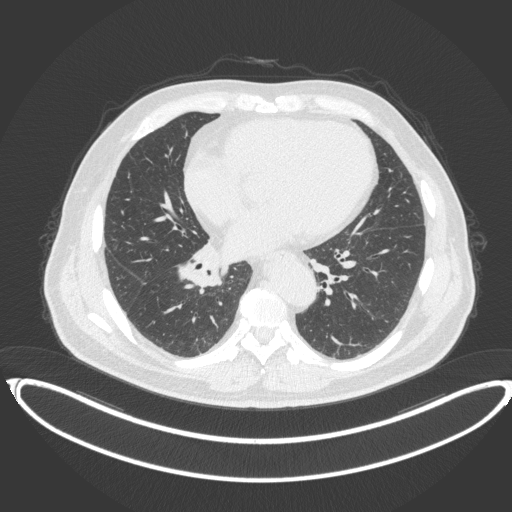
Chest CT, one axial slice. Position 172 of 383 along the scan axis. Lung window (W 1500 / L -600 HU). 1 mm slice thickness. 512 × 512 image matrix, field of view 448 × 448 mm. Patient: male, 61 years. Case-level facts recorded for this patient, not image findings: clinical TNM (as recorded): T1b N1 M0.
Outlined on this slice (bounding box drawn by a radiologist):
- lung tumour (recorded histology: squamous cell carcinoma): bounding box (x1, y1, x2, y2) in pixels: (173, 238, 223, 291)